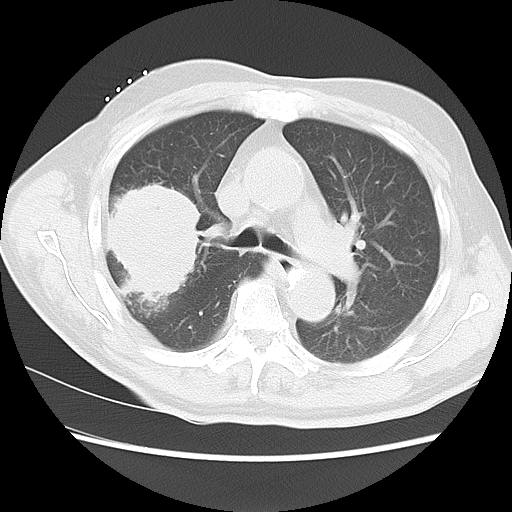
Chest CT, one axial slice. Position 9 of 15 along the scan axis. 120 kVp. Lung window (W 1500 / L -600 HU). 5 mm slice thickness. 512 × 512 image matrix, field of view 350 × 350 mm. Patient: male, 68 years. From the clinical record (not read from this slice): clinical TNM (as recorded): T4 N3 M0.
Annotated regions visible in this slice (rectangle marked by the reading radiologist):
- lung tumour (recorded histology: squamous cell carcinoma): bounding box [x1, y1, x2, y2] px = [106, 169, 204, 316]